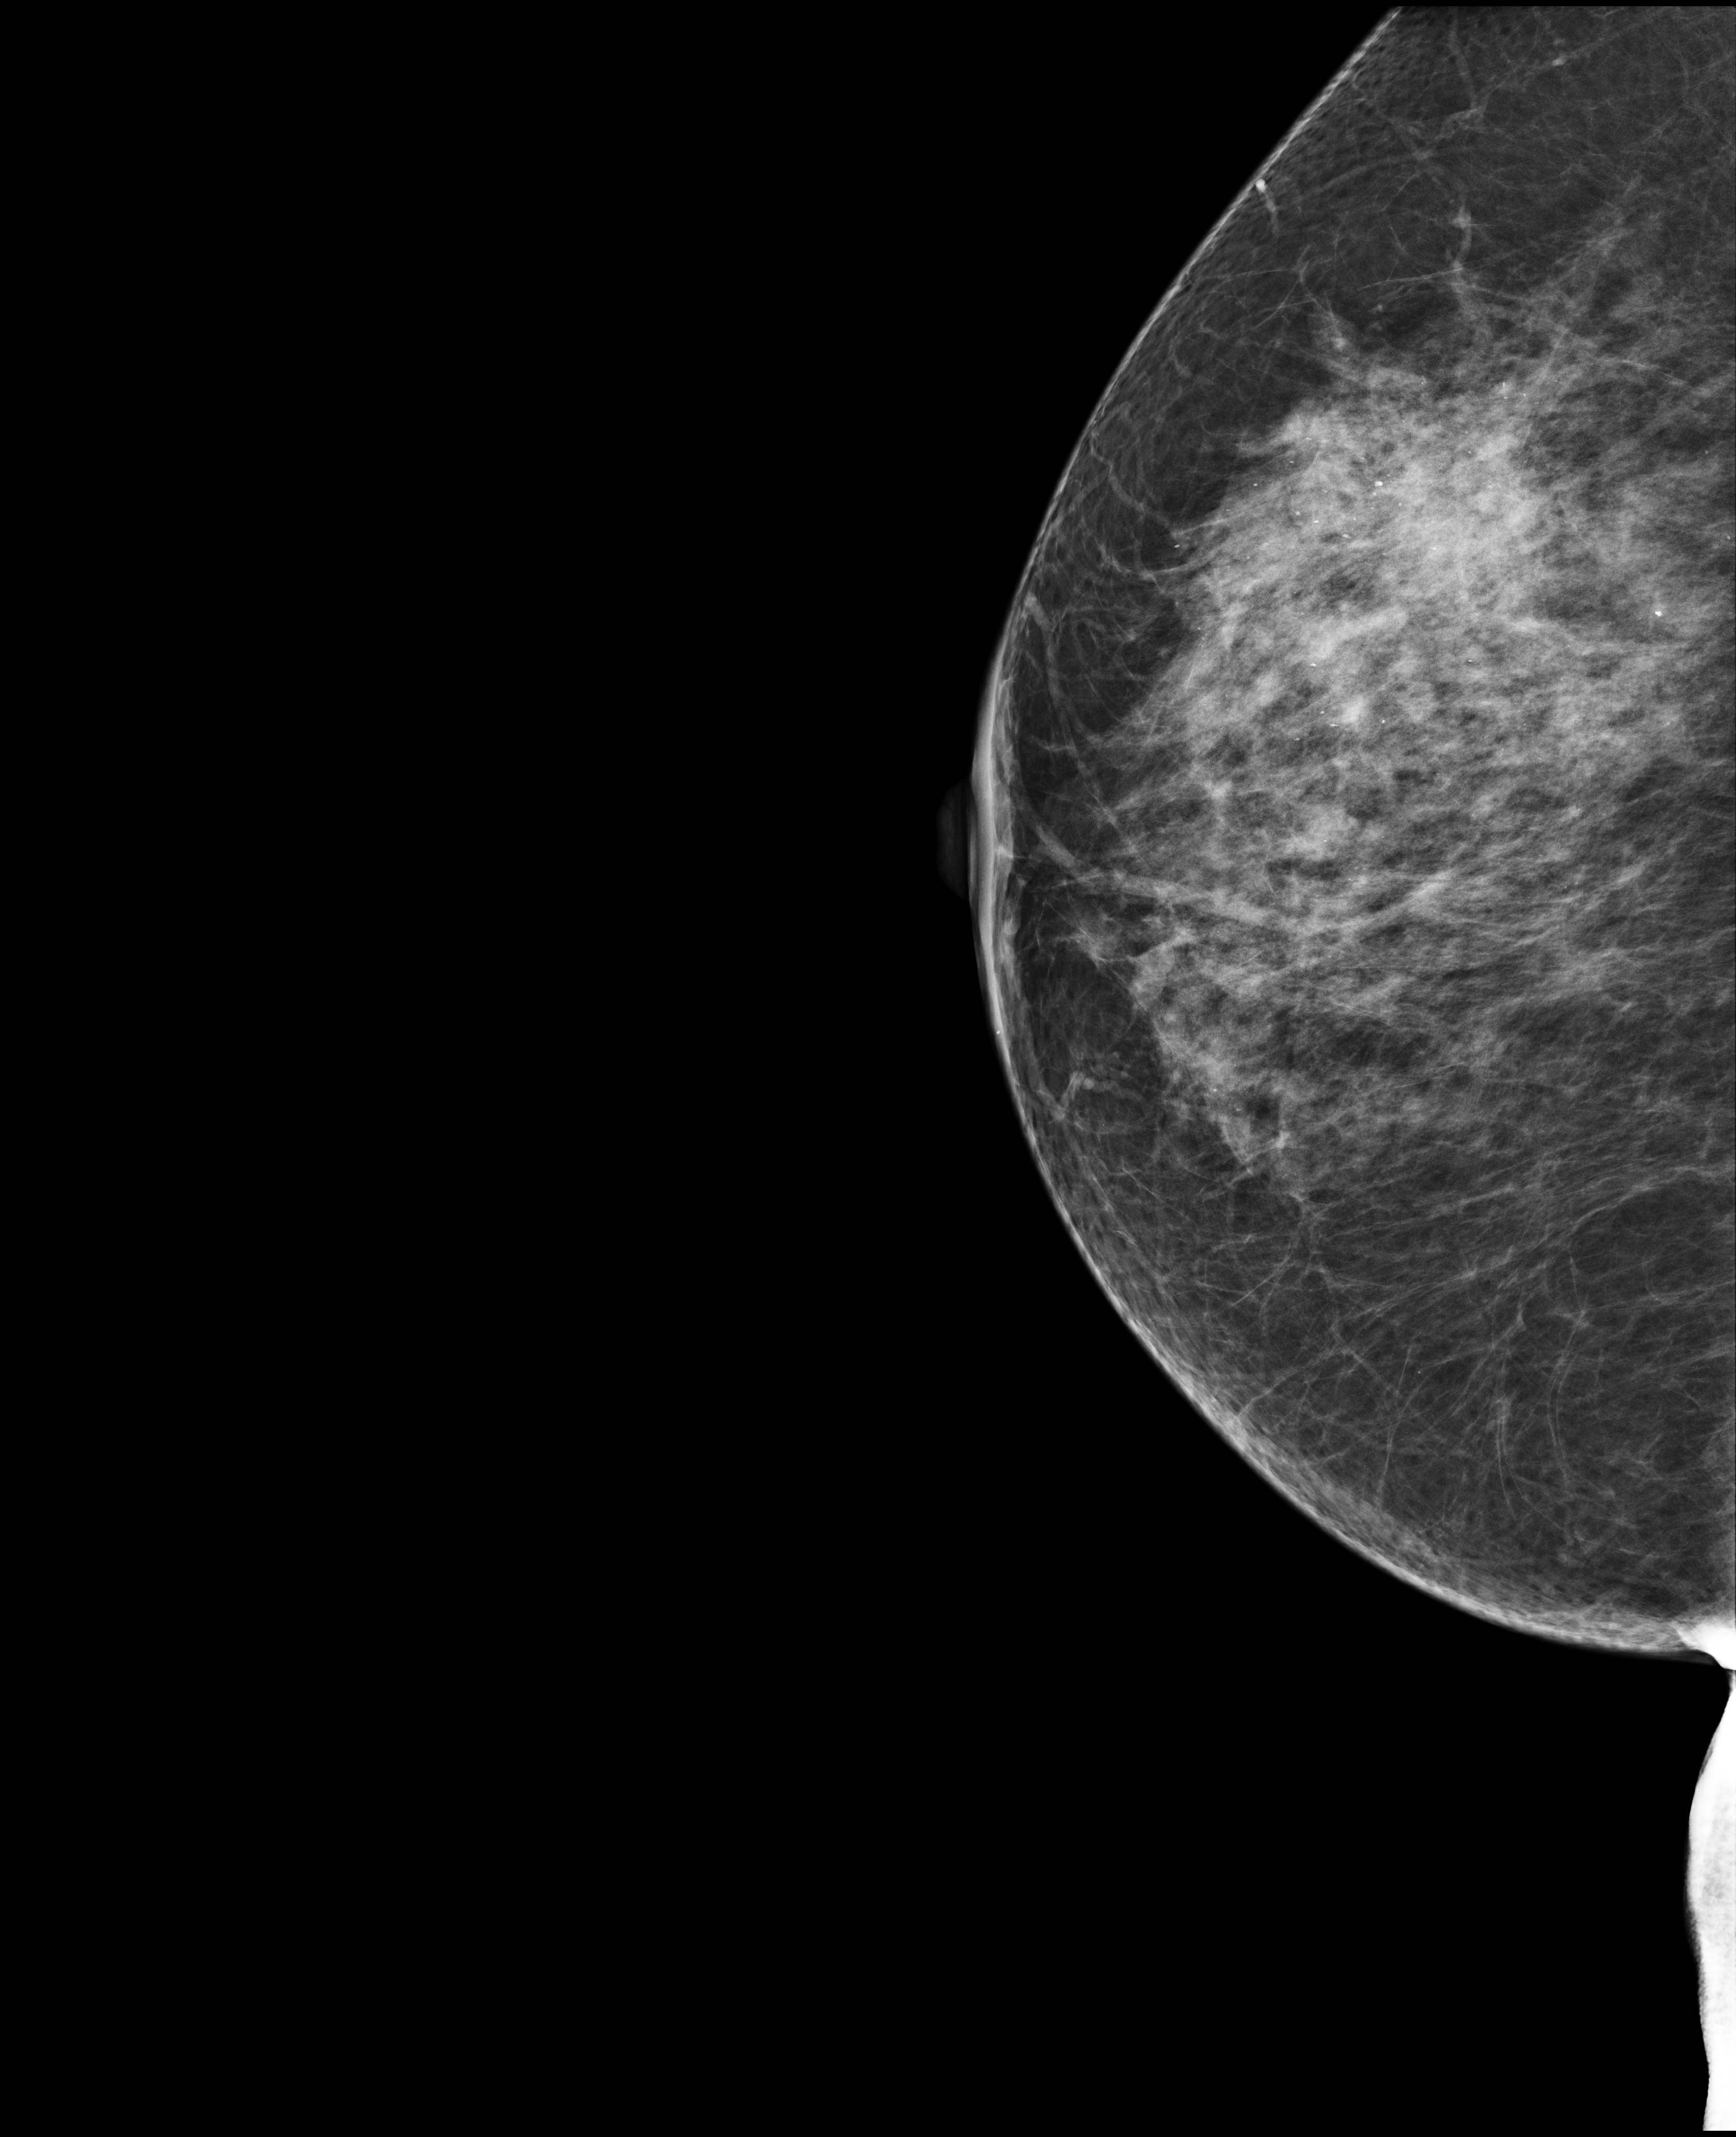
Digital mammogram (FFDM); right breast; ML view; diagnostic work-up study. Patient aged 71 years (female).
Final BI-RADS category for the screening round (tomosynthesis exam, both breasts): category 1.